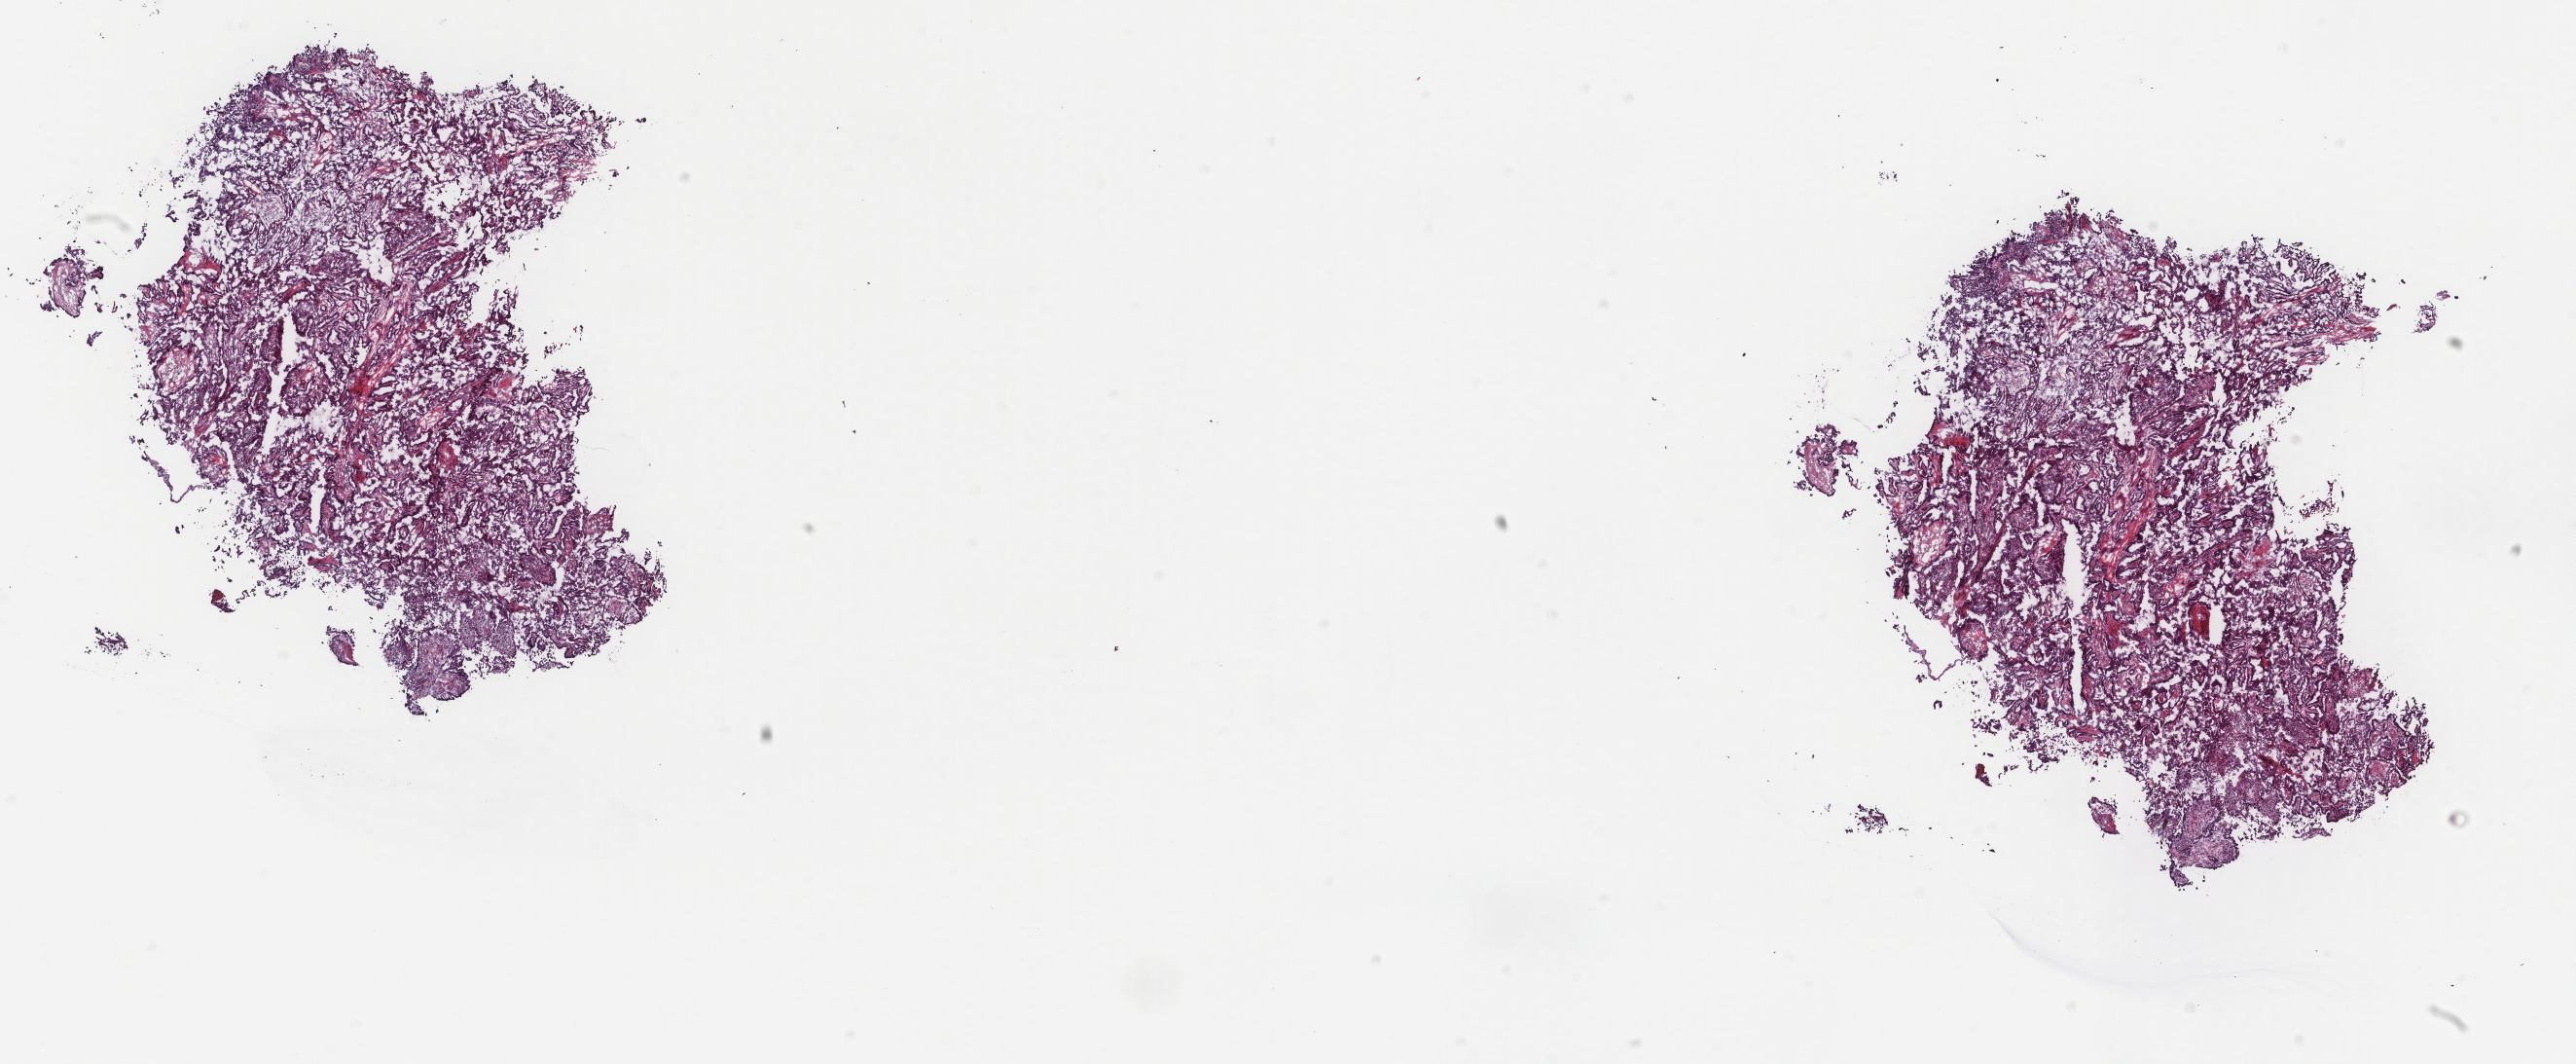
Whole-slide histology image, H&E-stained — shown as a low-resolution overview of the whole scanned area (about 21.0 x 8.7 mm, from a 40x scan); frozen section from the top of the tissue portion; primary tumour sample from the thyroid. Patient: female, age at initial diagnosis 36 years. Slide review estimates, as recorded: tumour cells 100%, tumour nuclei 75%, normal cells 0%, stromal cells 0%, necrosis 0%. Infiltration values recorded for this section: lymphocyte infiltration 0%, monocyte infiltration 0%, neutrophil infiltration 0%.
AJCC pathologic stage: I (5th edition). Diagnosis: Papillary adenocarcinoma, NOS (thyroid gland). Laterality: right.